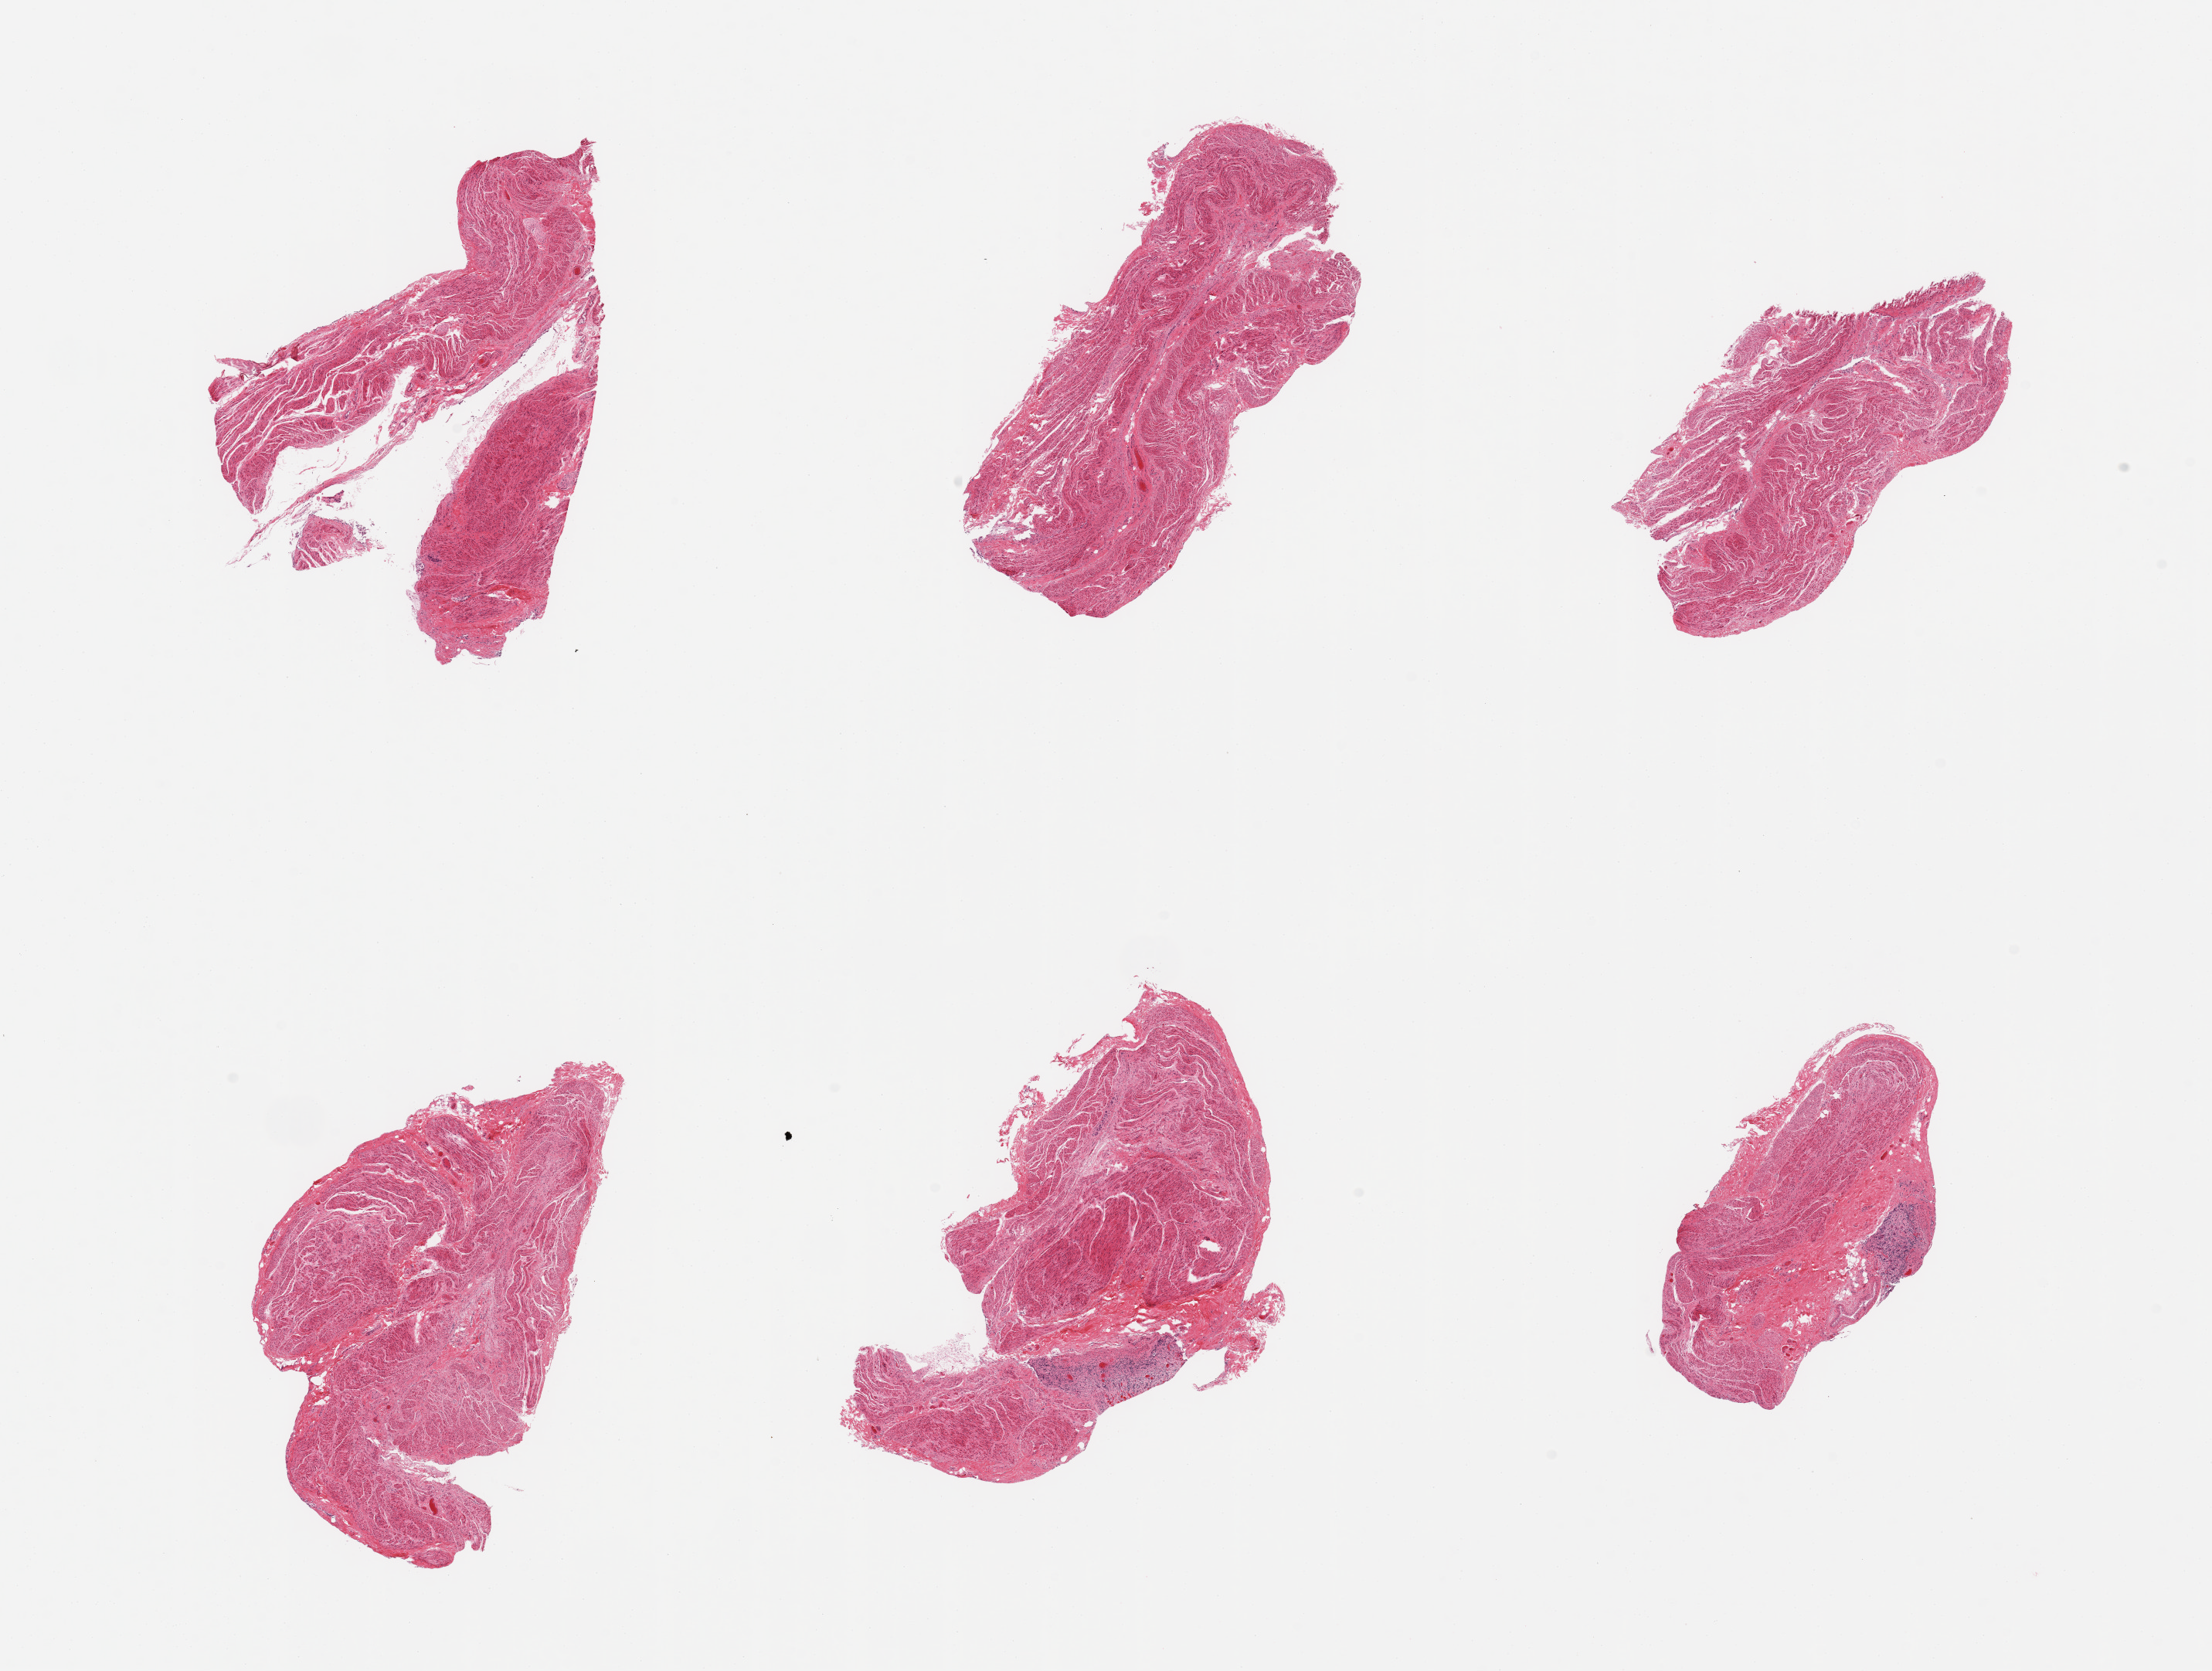
Digitized haematoxylin and eosin-stained section — low-resolution overview of the scanned area, about 22.6 x 17.1 mm (acquisition: 20x scan). PAXgene-fixed paraffin-embedded (PFPE) section. Target tissue: stomach. Donor tissue sample. Donor: male.
* review note (as recorded): 6 pieces; 95% muscularis propria with small foci of completely autolyzed mucosa